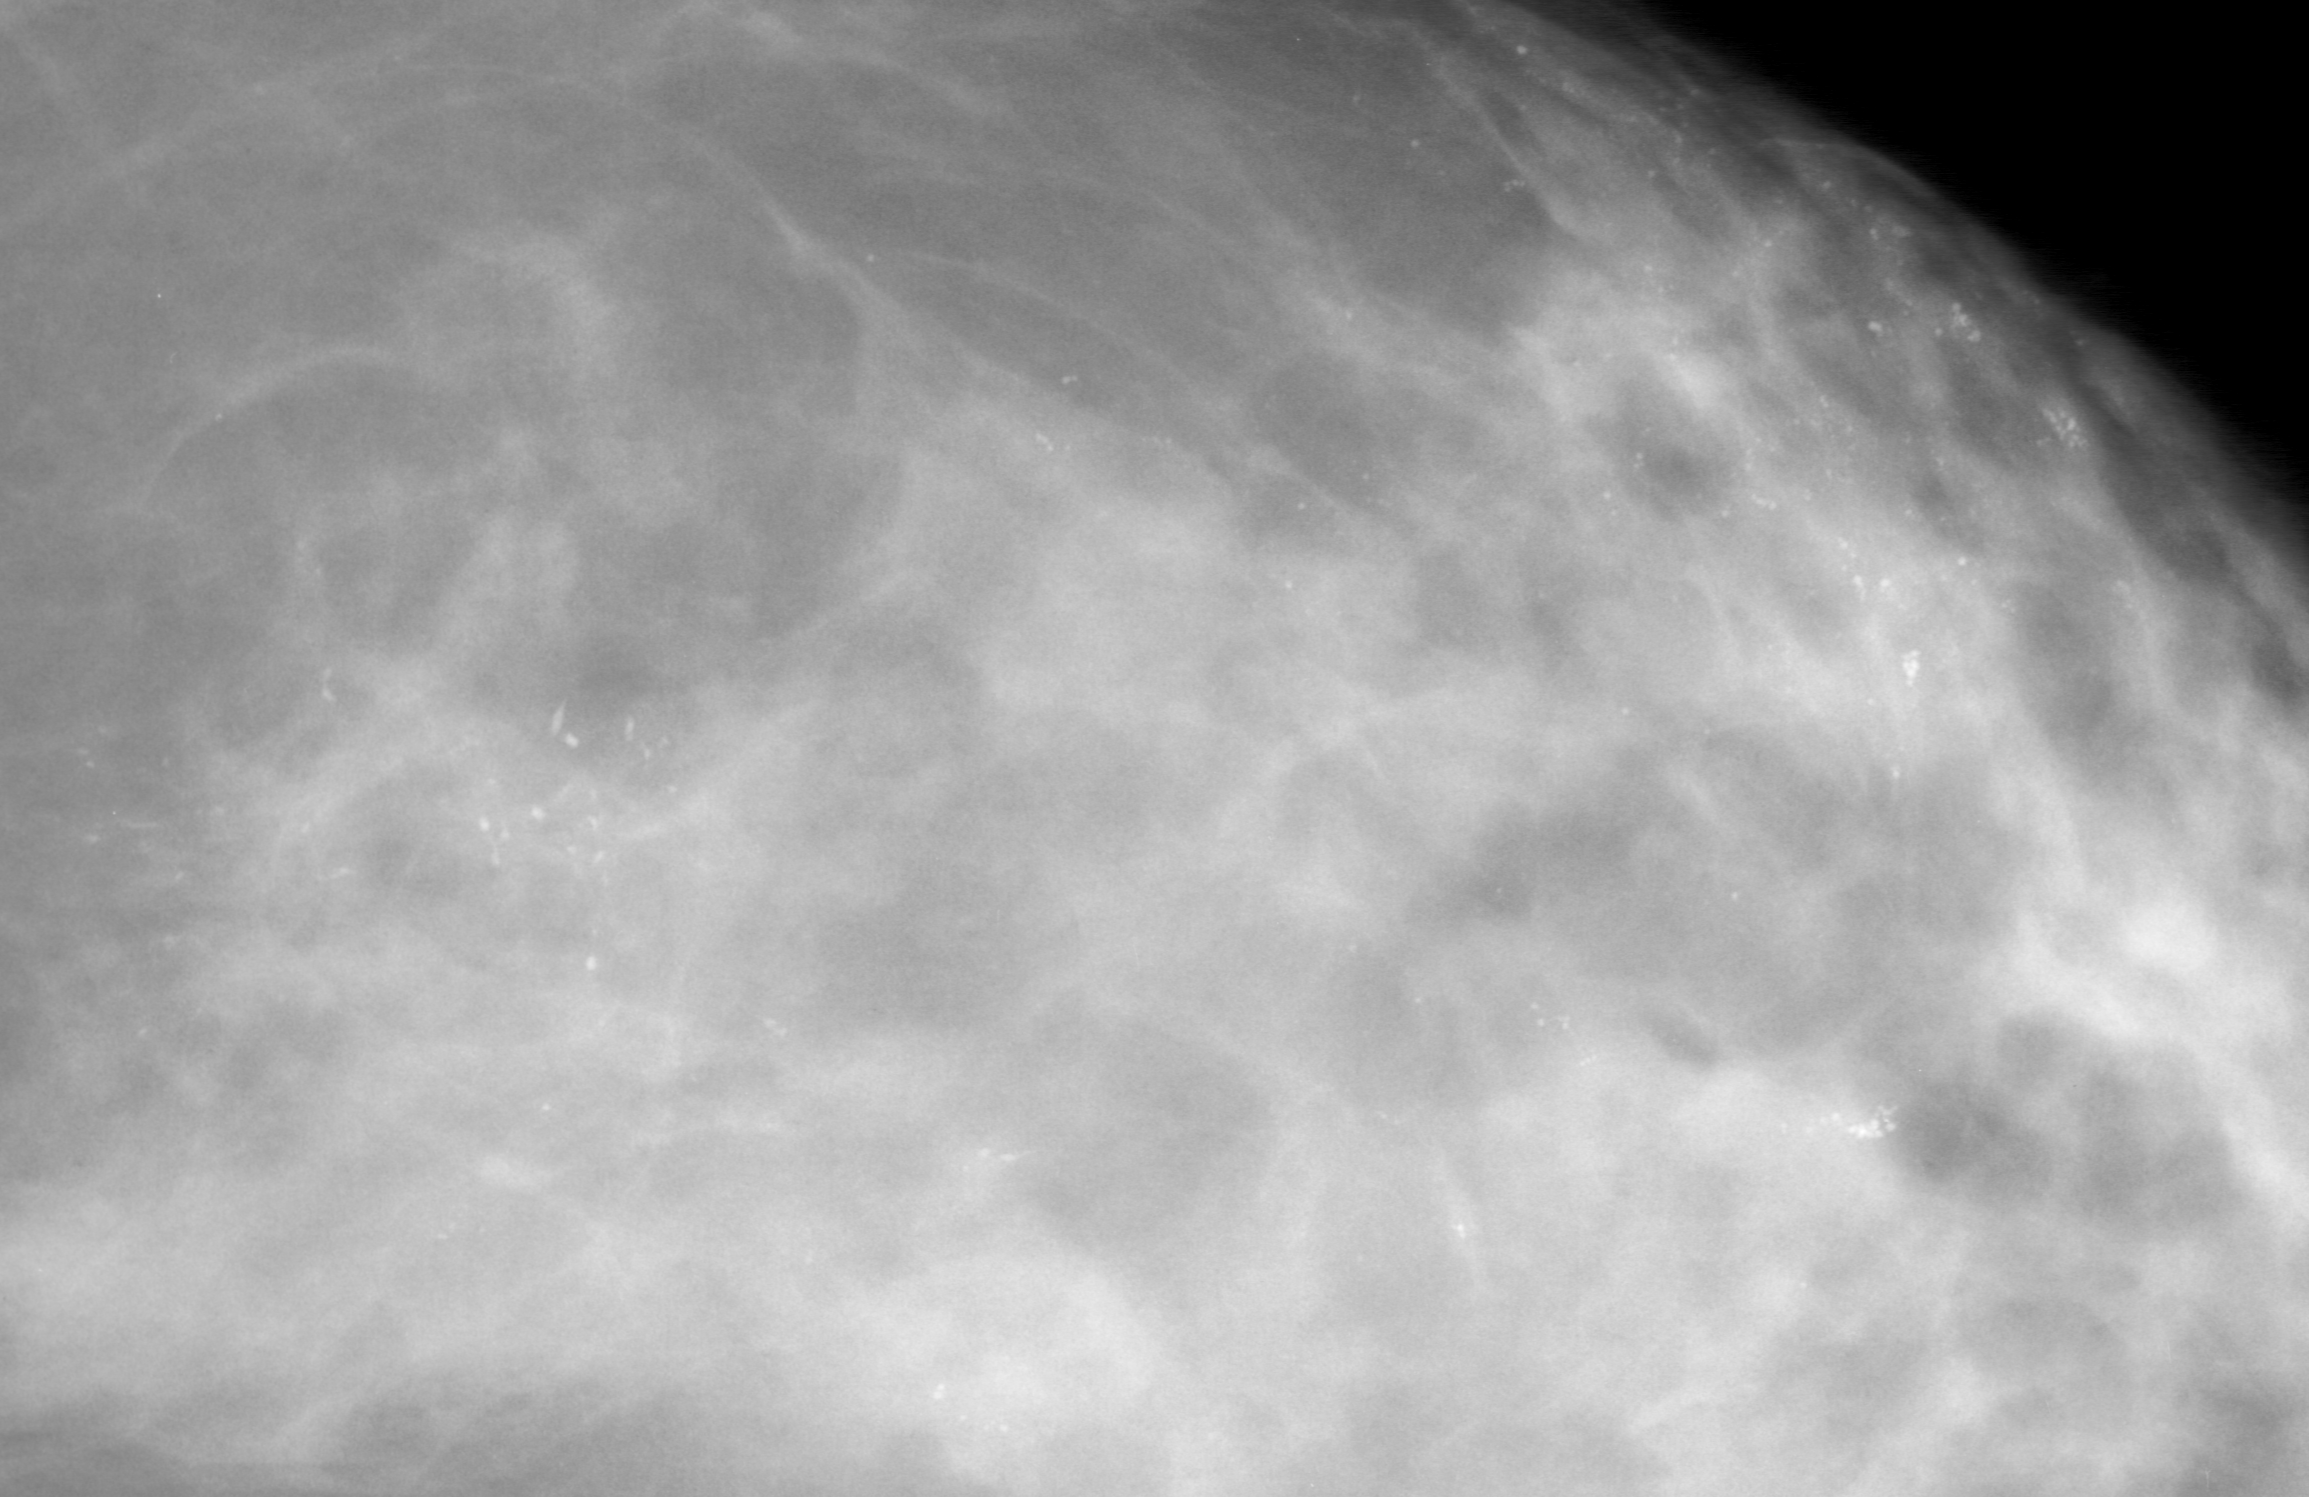
Region of interest cut from a scanned film mammogram (one marked finding), left breast, CC view.
Marked abnormality: calcifications, morphology pleomorphic, distribution regional; BI-RADS assessment category 5; pathology result (as recorded, not read from the image): malignant.